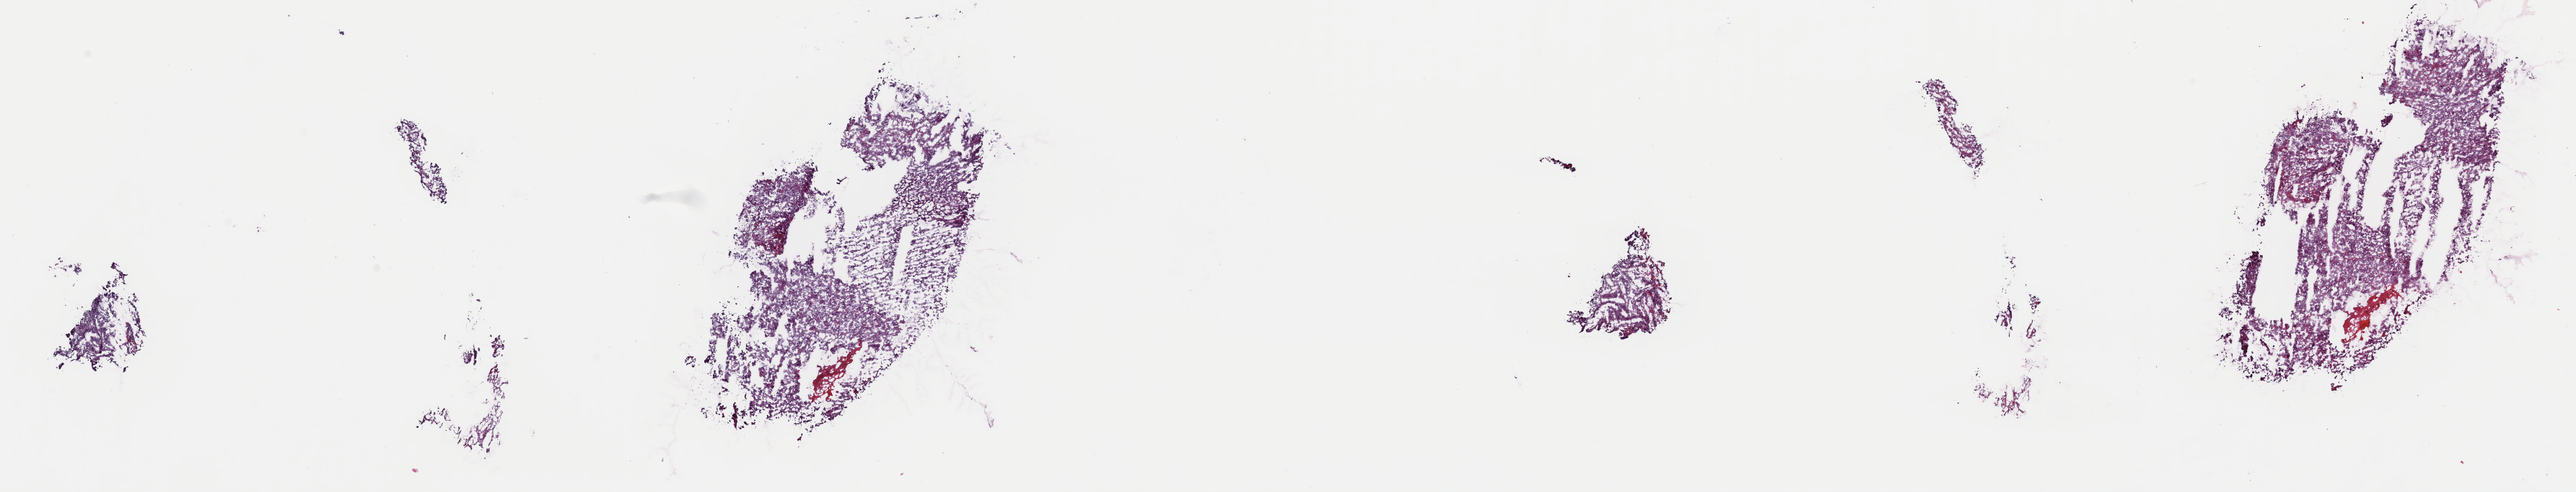
Whole-slide histology image, Hematoxylin and eosin (H&E) stained, shown as a low-resolution overview of the whole scanned area (about 28.2 x 5.4 mm), frozen section from the top of the tissue portion, primary tumour sample from the adrenal cortex. Patient: female, age at initial diagnosis 45 years. Pathologist review of this section (percent, as recorded): tumour cells 95%, tumour nuclei 90%, normal cells 0%, stromal cells 5%, necrosis 0%. Infiltration values recorded for this section: lymphocyte infiltration 0%, monocyte infiltration 0%, neutrophil infiltration 8%.
Pathologic diagnosis: Adrenal cortical carcinoma (cortex of adrenal gland). Lymph nodes positive (case pathology): 0 of 6 examined.